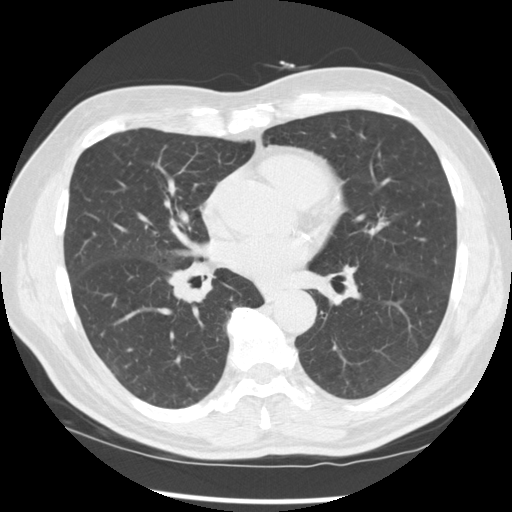
Low-dose screening chest CT, one axial slice. Slice 138 of 277 in the series (ordered by position). Reconstruction kernel STANDARD. 120 kVp. Lung window (W 1500 / L -600 HU). 512 × 512 image matrix.
Outlined on this slice (outlined manually by an expert reader):
- lesion 1 (tumor, middle lobe of right lung): bounding box [x1, y1, x2, y2] px = [168, 270, 207, 303]